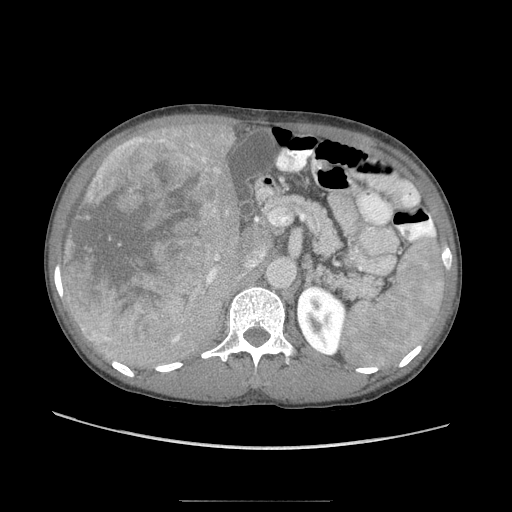
Contrast-enhanced abdominal CT (liver protocol), one axial slice; slice 47 of 103 in the series (ordered by position); 120 kVp; soft-tissue window (W 400 / L 40 HU); 2.5 mm slice thickness; 512 × 512 image matrix, field of view 380 × 380 mm. From the clinical record (not read from this slice): diagnosis: hepatocellular carcinoma (patient treated with transarterial chemoembolisation; whether this scan precedes or follows treatment is not stated here); TNM stage (as recorded): Stage-IIIA; Child-Pugh class: A; tumour nodularity: multinodular.
Annotated regions visible in this slice (semi-automatic segmentation, software-assisted and operator-edited):
- liver parenchyma outside the tumour (the mass and vessels are separate outlines, so this box may not span the whole liver): bounding box <63,121,243,370> (left, top, right, bottom; pixels)
- mass: <61,125,221,348>
- liver vessels: <192,250,224,299>